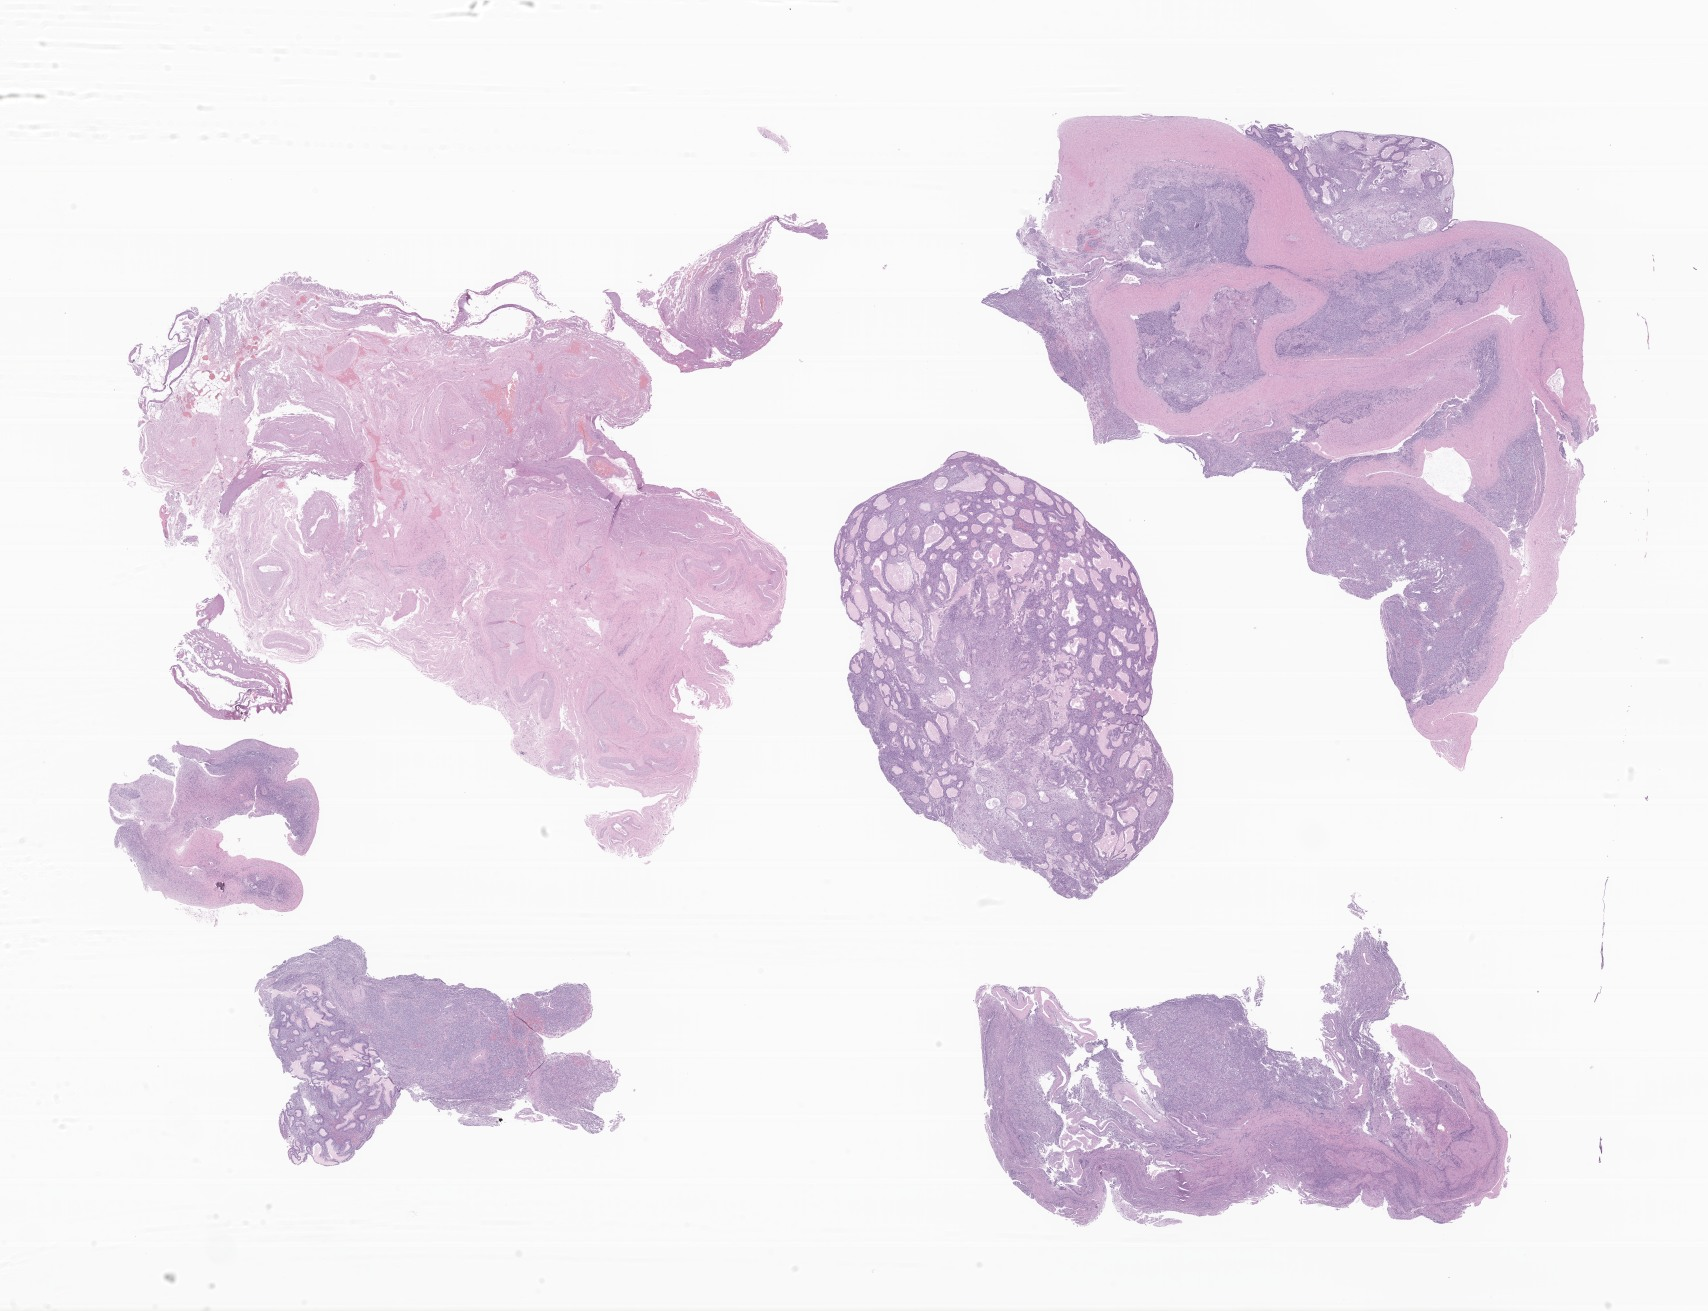
Digitized hematoxylin and eosin (H&E)-stained section of tumor tissue from the ovary, shown as a low-resolution overview of the whole scanned area (about 28.8 x 22.1 mm), formalin-fixed, paraffin-embedded (FFPE) tissue. Patient female; age 275 months (22 years 11 months).
Diagnosis (ICD-O-3 morphology term): Sertoli-Leydig cell tumor, mod diff, with heterologous elements.